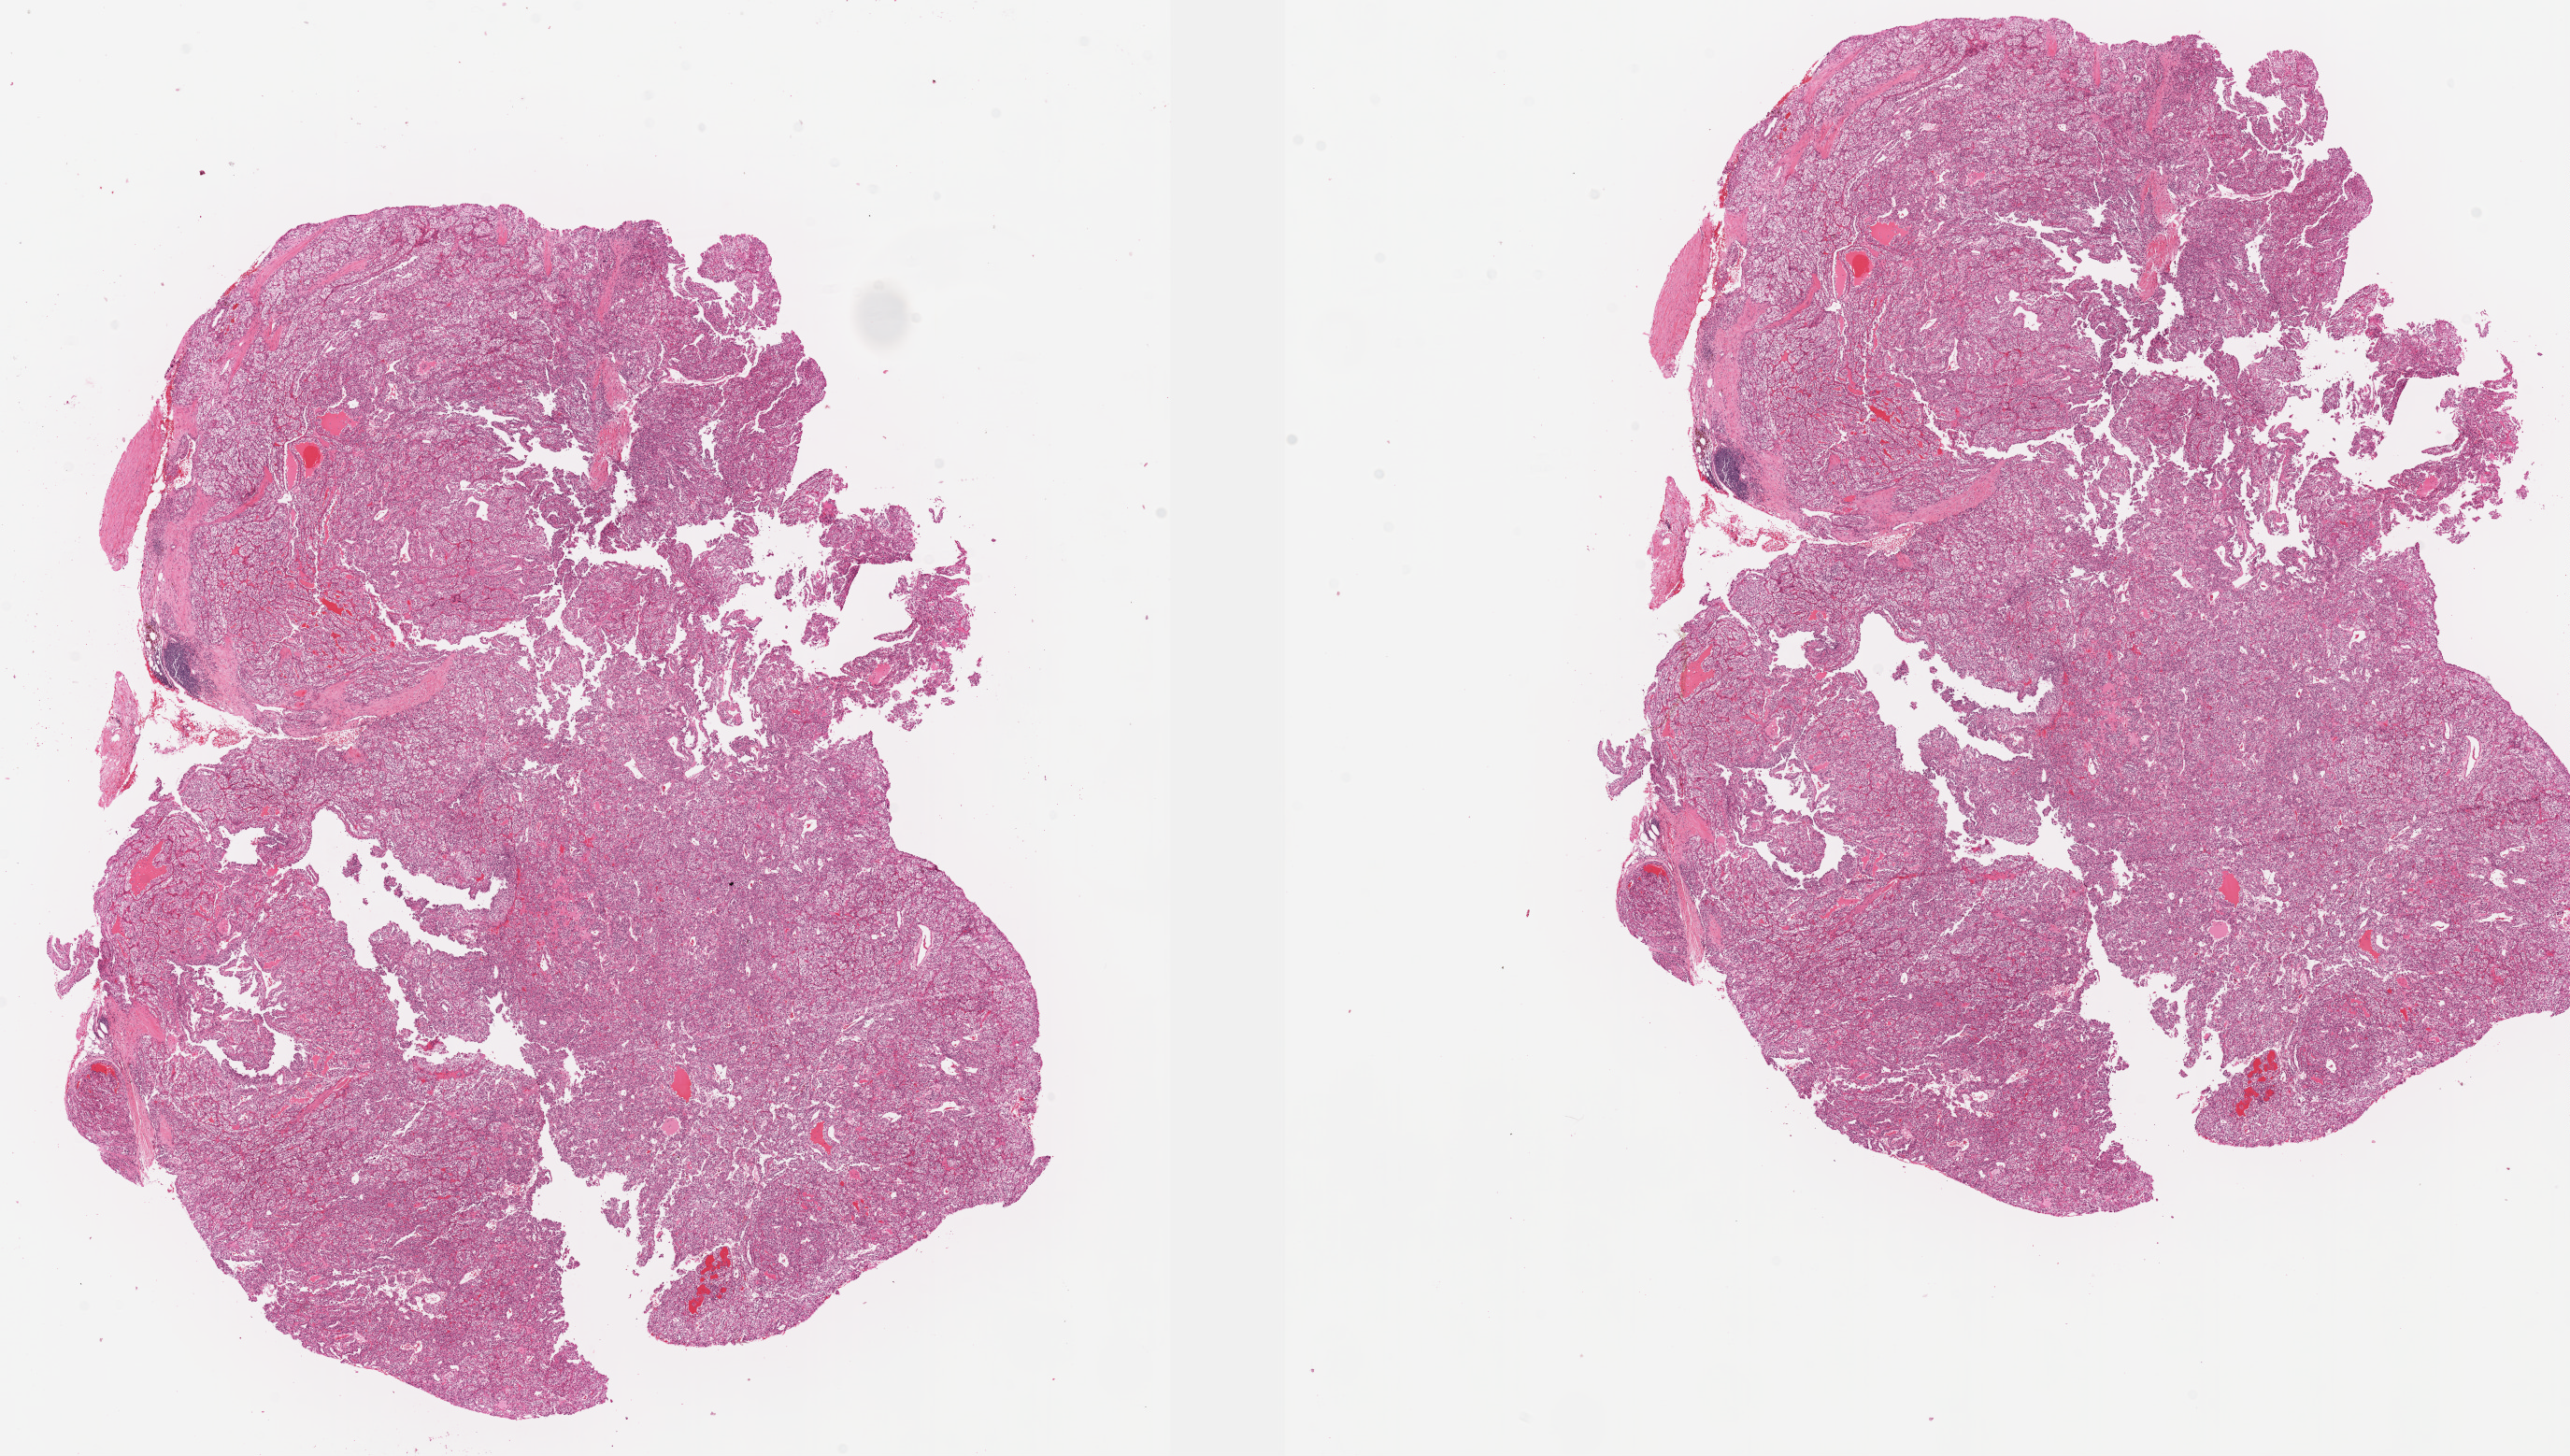
H&E-stained whole-slide image — low-resolution overview of the scanned area, about 21.7 x 12.3 mm (acquisition: 20x scan); formalin-fixed paraffin-embedded (FFPE) diagnostic section; primary tumour sample from the kidney. Female, age 61 years at initial diagnosis. Histologic grade: G3 (poorly differentiated).
Pathologic diagnosis: Clear cell adenocarcinoma, NOS. AJCC pathologic stage: I (7th edition). TNM: T1a N0 M0.